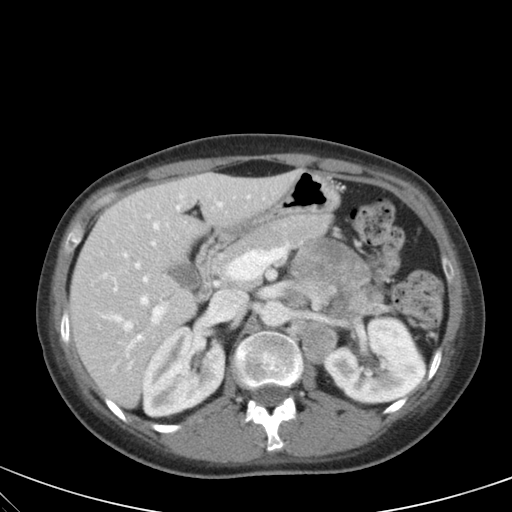
Contrast-enhanced abdominal CT, one axial slice; position 32 of 59 along the scan axis; 120 kVp; intravenous contrast given; soft-tissue window (W 400 / L 40 HU); 4 mm slice thickness; 512 × 512 image matrix, field of view 350 × 350 mm. Female patient, age 28 years. From the clinical record (not read from this slice): diagnosis: adrenocortical carcinoma; tumour side: left adrenal; tumour size at pathology: 7 cm; Ki-67 index: 40 %; stage (as recorded): 4.
Annotated regions visible in this slice (semi-automatically segmented with operator editing):
- mass: bounding box <290,241,382,318> (left, top, right, bottom; pixels)